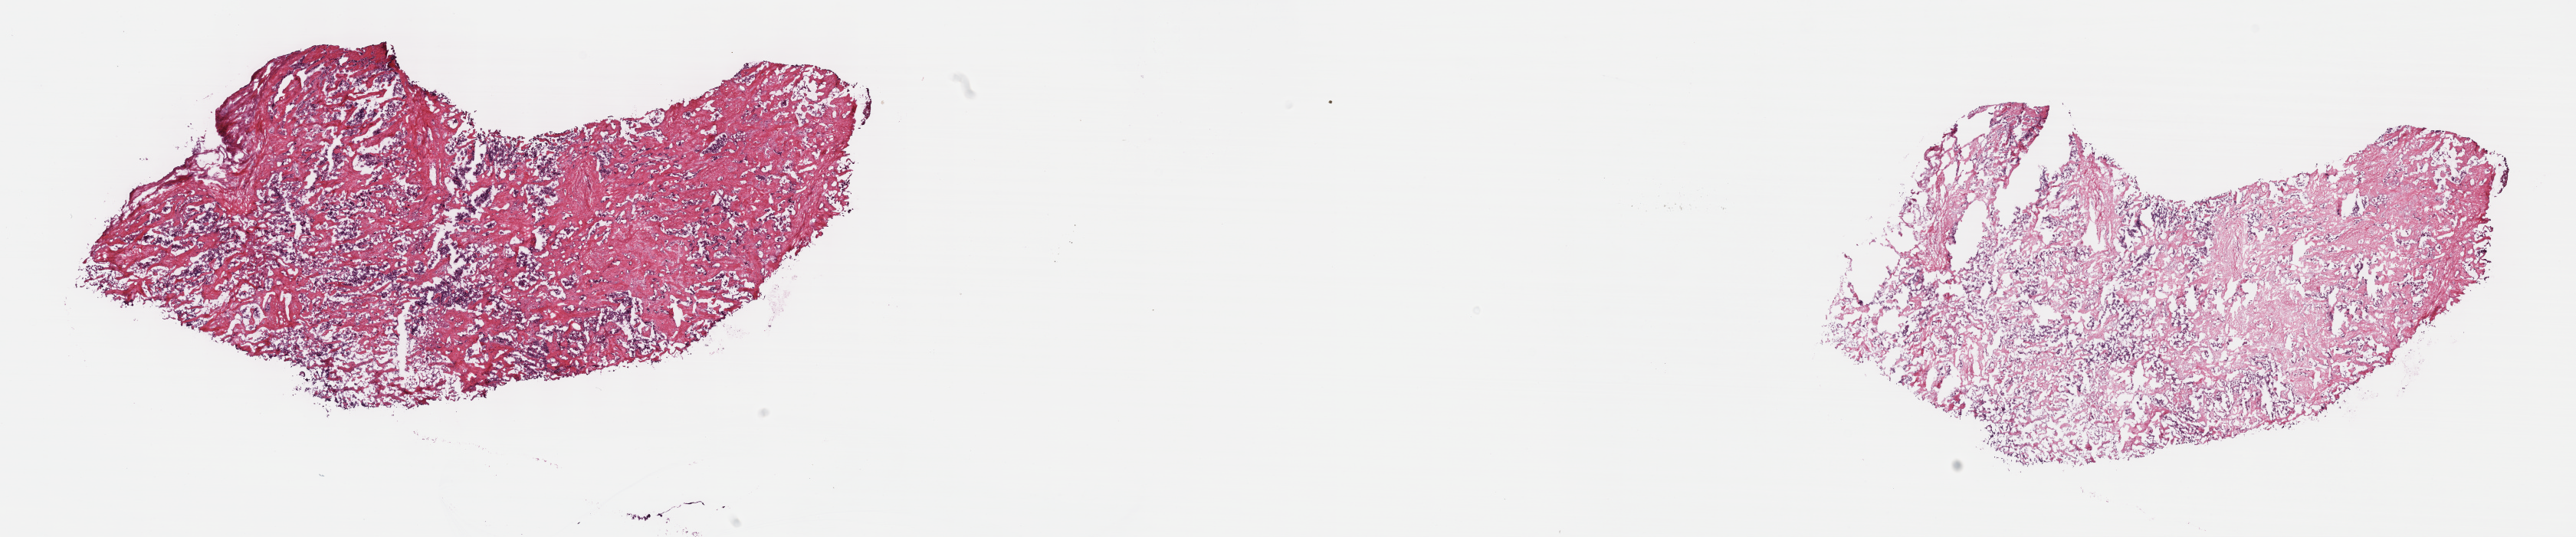
Digitized H&E-stained tissue section (whole slide), a low-resolution overview of the entire scanned area, about 27.2 x 5.7 mm (slide scanned at 40x); frozen section from the top of the tissue portion; sample: primary tumour, bile duct. Patient: female, age at initial diagnosis 74 years. Histologic grade: G2 (moderately differentiated). Pathologist review of this section (percent, as recorded): tumour cells 25%, tumour nuclei 80%, normal cells 0%, stromal cells 75%, necrosis 0%. Inflammatory infiltration, as recorded: lymphocyte infiltration 0%, monocyte infiltration 0%, neutrophil infiltration 0%.
- diagnosis: Cholangiocarcinoma (intrahepatic bile duct)
- AJCC pathologic stage: III (7th edition)